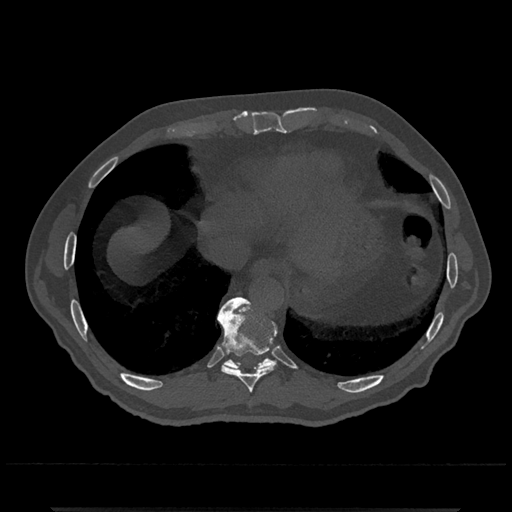
CT including the spine, one axial slice. Position 593 of 797 along the scan axis. Reconstruction kernel Br40s/3. 120 kVp. Bone window (W 1800 / L 400 HU). 512 × 512 image matrix. Patient: male, 67 years. Case-level facts recorded for this patient, not image findings: primary cancer: prostate.
Annotated regions visible in this slice (semi-automatic segmentation, software-assisted and operator-edited):
- T10 vertebra: bounding box (x1, y1, x2, y2) in pixels: (217, 297, 276, 370)
- T9 vertebra: (217, 298, 278, 393)